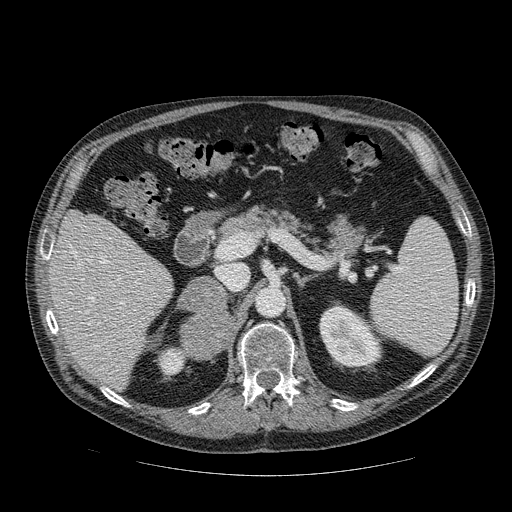
Contrast-enhanced abdominal CT, one axial slice; position 53 of 111 along the scan axis; 120 kVp; intravenous contrast given; soft-tissue window (W 400 / L 40 HU); 512 × 512 image matrix. Patient: male, 56 years. From the clinical record (not read from this slice): diagnosis: adrenocortical carcinoma; tumour side: right adrenal; tumour size at pathology: 9 cm; Ki-67 index: 48 %.
Annotated regions visible in this slice (semi-automatically segmented with operator editing):
- mass: bounding box [x1, y1, x2, y2] px = [180, 276, 233, 358]